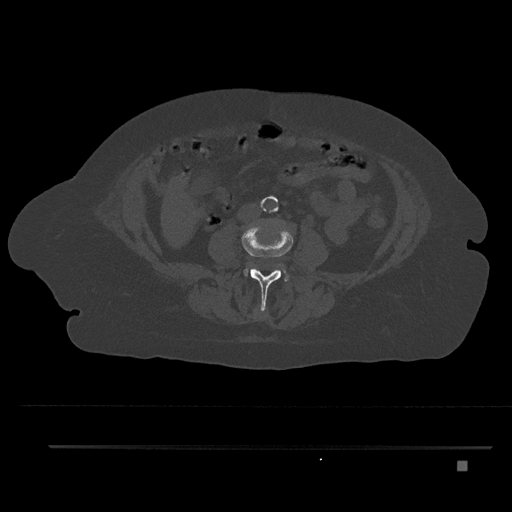
CT including the spine, one axial slice; position 117 of 797 along the scan axis; 120 kVp; bone window (W 1800 / L 400 HU); 0.5 mm slice thickness; 512 × 512 image matrix. Patient: female, 76 years. Case-level facts recorded for this patient, not image findings: primary cancer: lung; vertebrae with lytic lesions (as recorded): T11, L3.
Annotated regions visible in this slice (semi-automatically segmented with operator editing):
- L2 vertebra: bounding box [x1, y1, x2, y2] px = [256, 308, 264, 315]
- L3 vertebra: [242, 224, 293, 309]
- L4 vertebra: [247, 263, 289, 281]